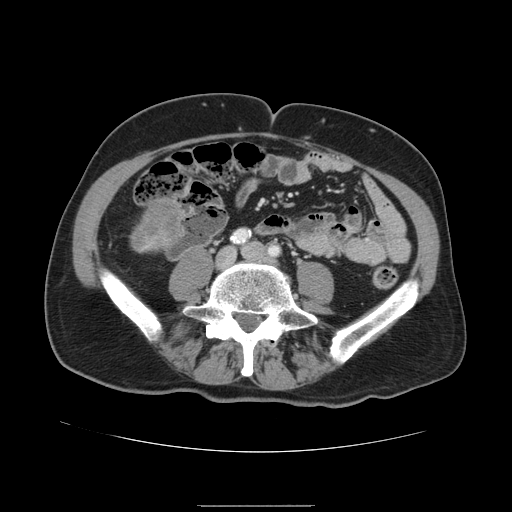
Contrast-enhanced abdominal CT, one axial slice; slice 8 of 168 in the series (ordered by position); intravenous contrast given; soft-tissue window (W 400 / L 40 HU); 2.5 mm slice thickness; 512 × 512 image matrix, field of view 386 × 386 mm. Male patient, age 74 years. Case-level facts recorded for this patient, not image findings: diagnosis: colorectal cancer liver metastases, imaged before liver resection; multiple liver metastases: no; largest metastasis: 14.5 cm.
Annotated regions visible in this slice (manually delineated by an expert):
- liver: bounding box (x1, y1, x2, y2) in pixels: (130, 197, 187, 253)
- liver metastasis: (132, 200, 181, 247)